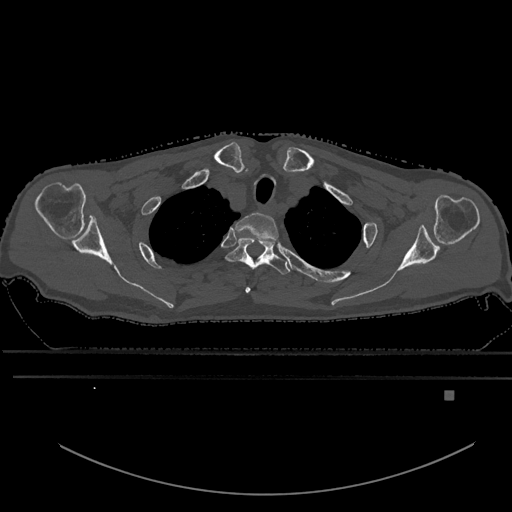
CT including the spine, one axial slice. Slice 506 of 969 in the series (ordered by position). Bone window (W 1800 / L 400 HU). 0.5 mm slice thickness. 512 × 512 image matrix, field of view 456 × 456 mm. Male patient, age 82 years. From the clinical record (not read from this slice): primary cancer: prostate.
Structures marked on this image (semi-automatic segmentation, software-assisted and operator-edited):
- T1 vertebra: box from (x=235, y=212) to (x=279, y=293) px
- T2 vertebra: (x=226, y=238)–(x=290, y=292)